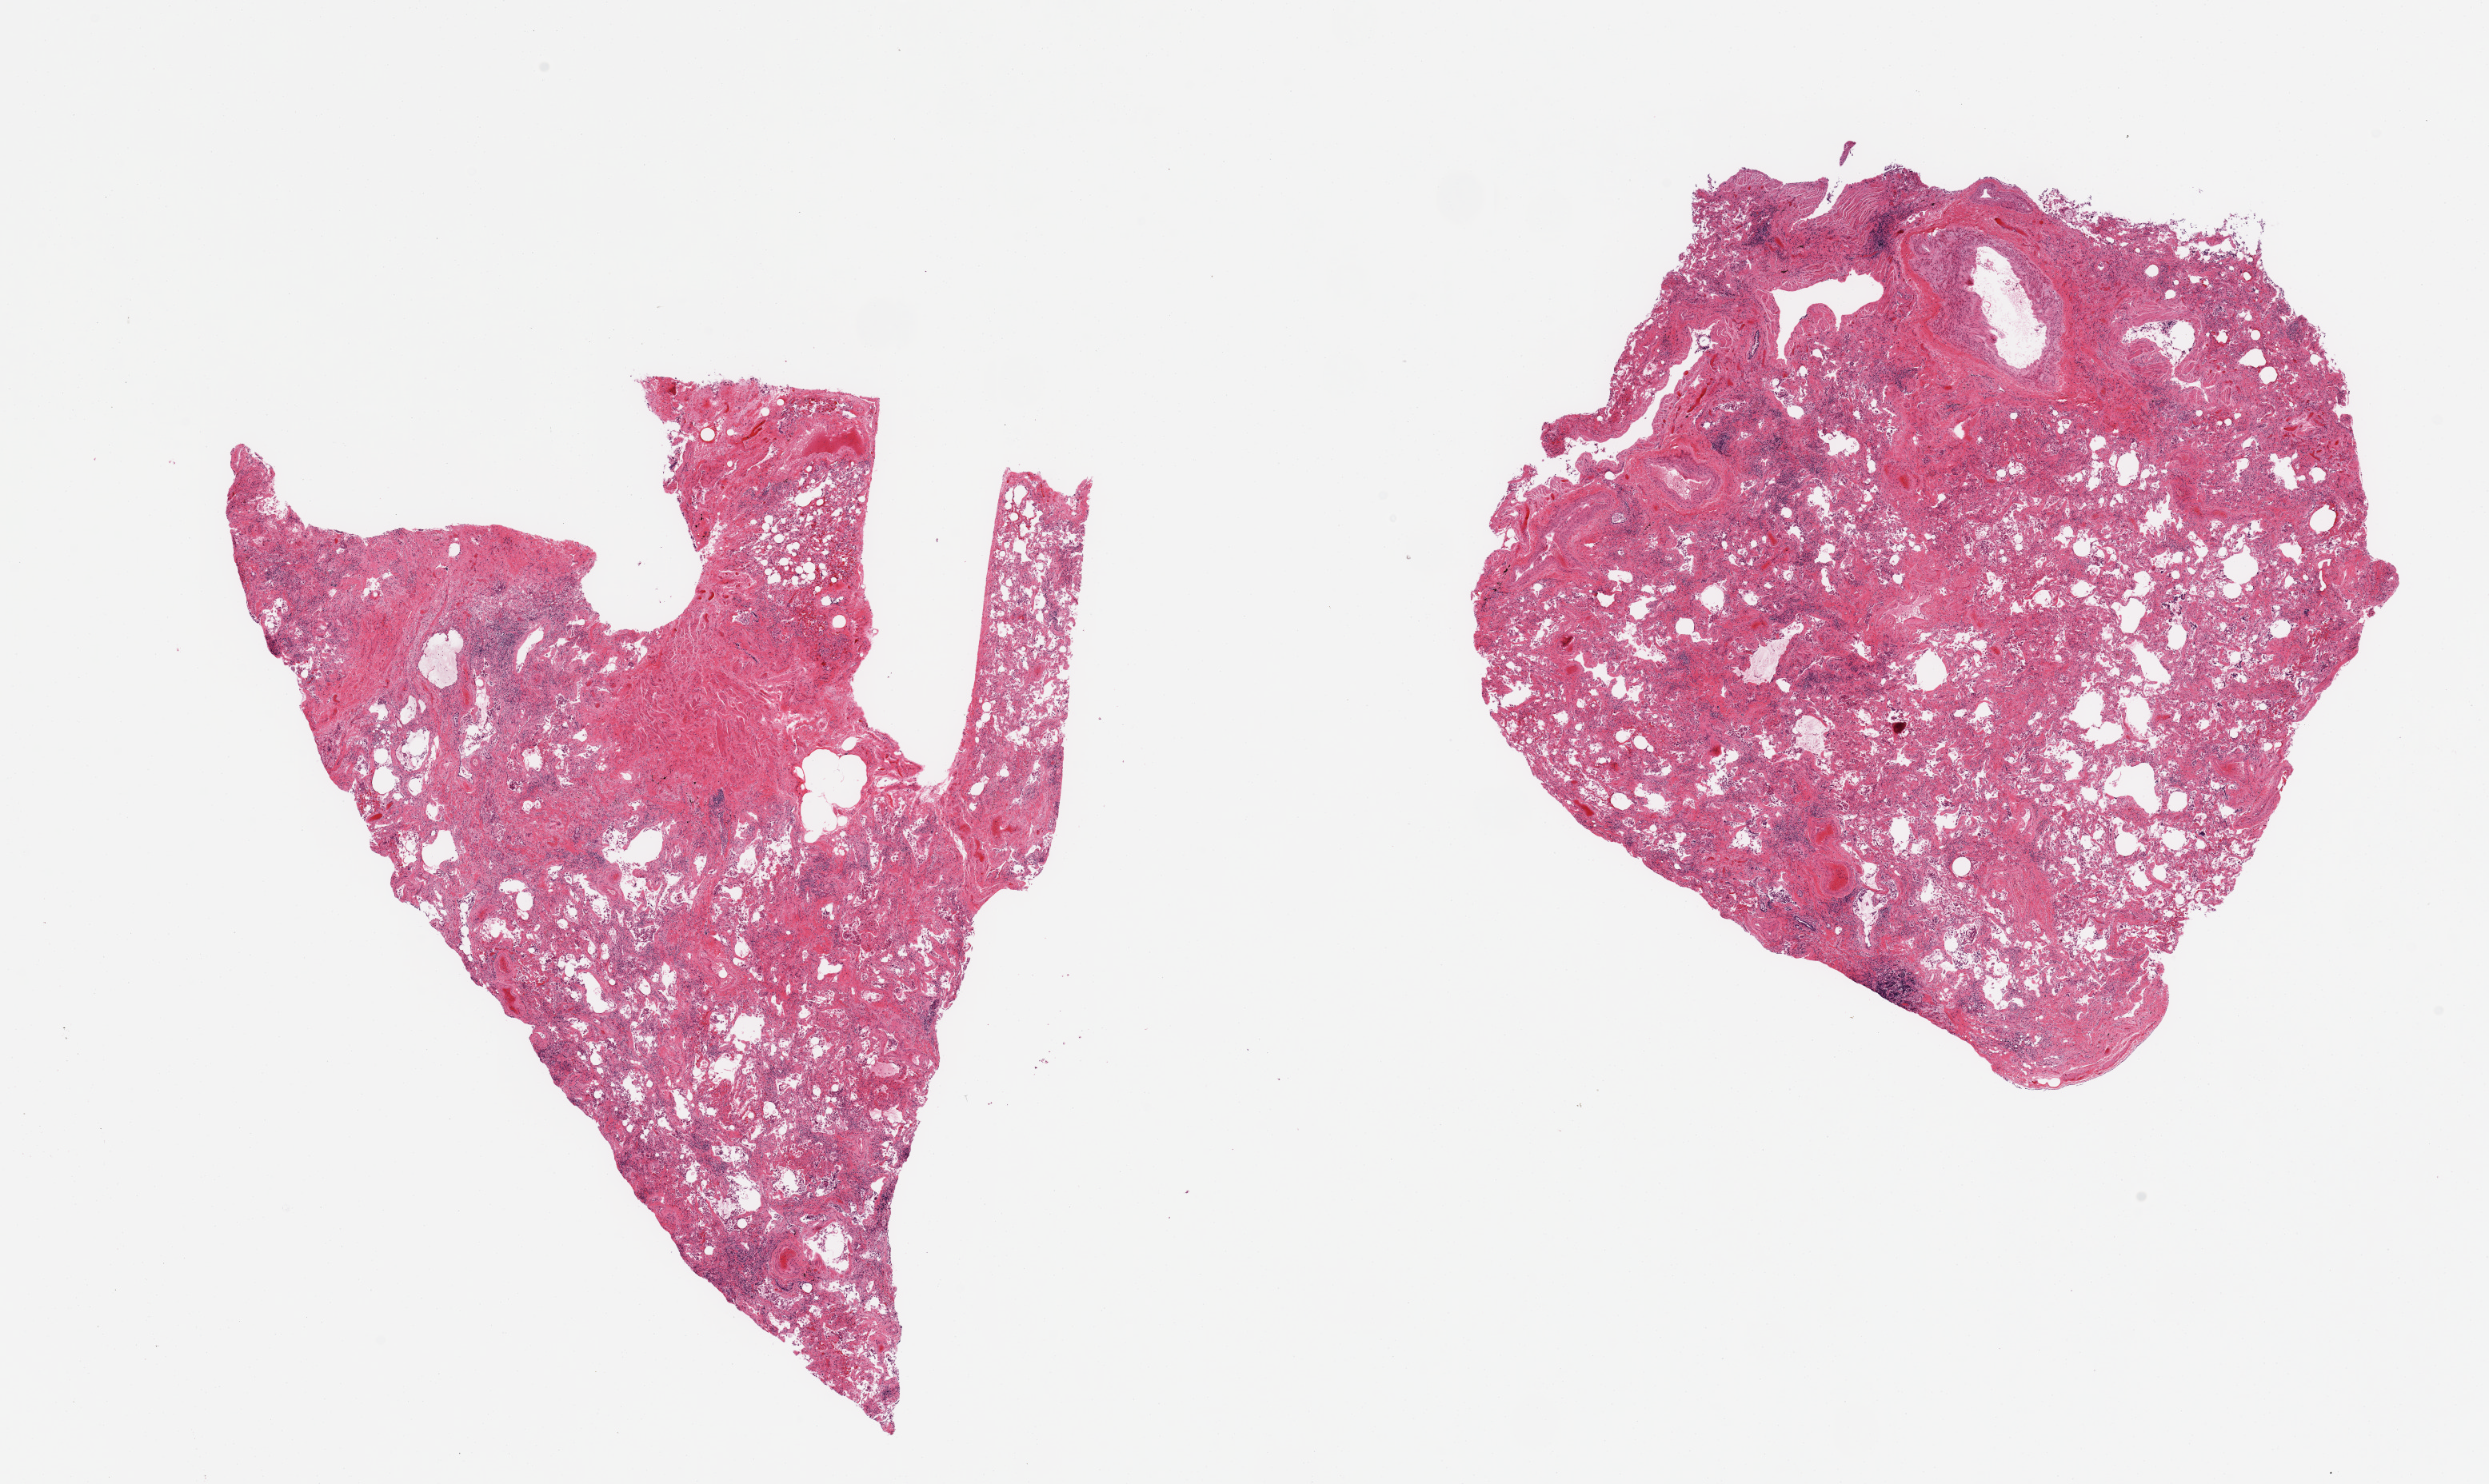
Whole-slide image, H&E stain — a low-resolution overview of the entire scanned area, about 24.6 x 14.7 mm; PAXgene-fixed, paraffin-embedded tissue; section of lung (target tissue); tissue donor sample.
Reviewer comment on this tissue sample: 2 pieces; severe interstitial fibrosis (correlates with clinical diagnosis); may be of limited use.